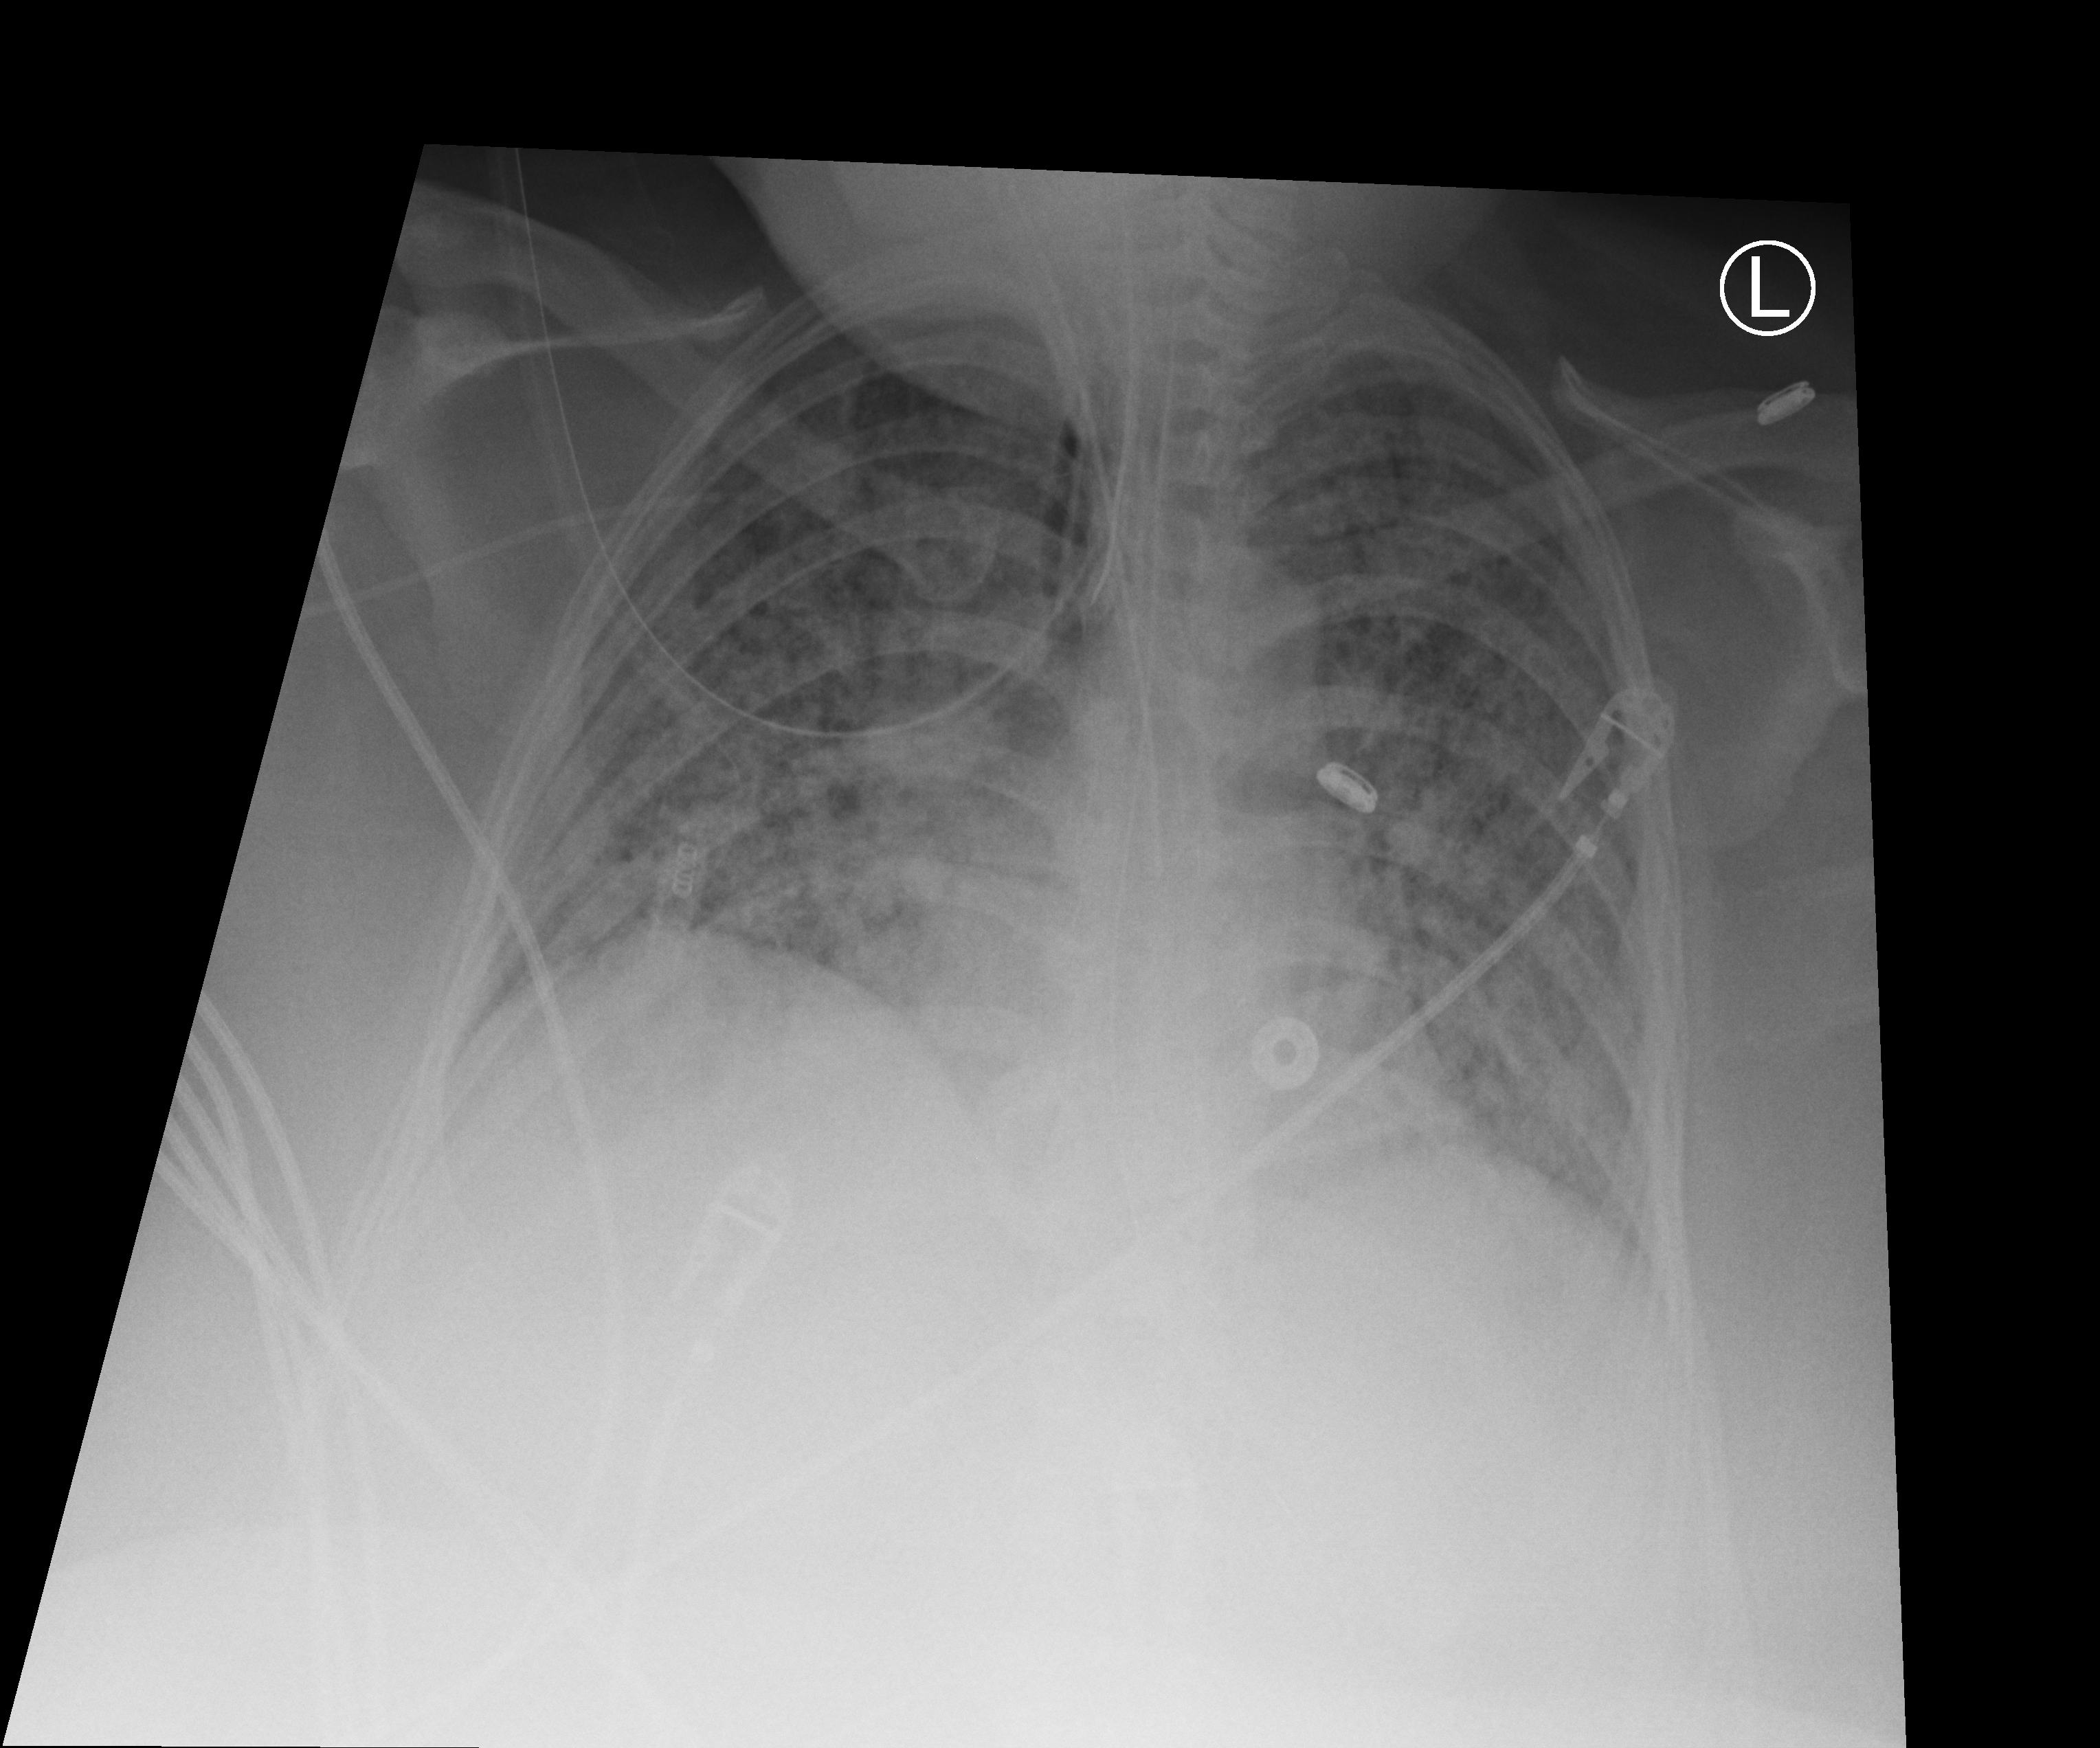
Portable chest radiograph, anteroposterior (AP) projection. Female patient hospitalised with COVID-19, age 18–59 years.
Hospital-stay facts (about this admission, not read from this image; timing relative to this image not recorded): mechanically ventilated during this hospital stay: yes.